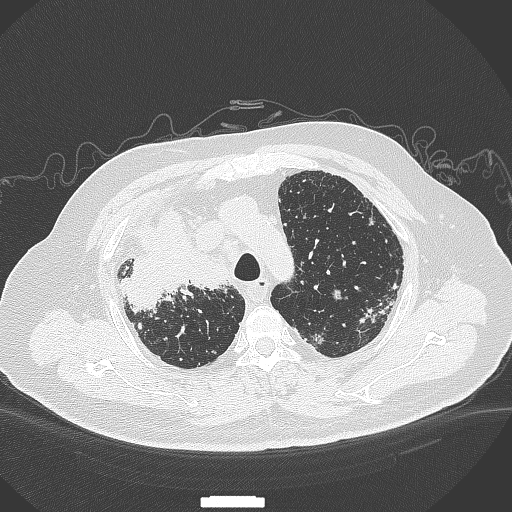
Chest CT, one axial slice. Position 280 of 384 along the scan axis. Reconstruction kernel B70f. 120 kVp. Lung window (W 1500 / L -600 HU). 1 mm slice thickness. 512 × 512 image matrix, field of view 400 × 400 mm. Male patient, age 69 years. Case-level facts recorded for this patient, not image findings: clinical TNM (as recorded): T4 N3 M1.
Outlined on this slice (rectangle marked by the reading radiologist):
- lung tumour (recorded histology: adenocarcinoma): bounding box (x1, y1, x2, y2) in pixels: (124, 206, 227, 317)